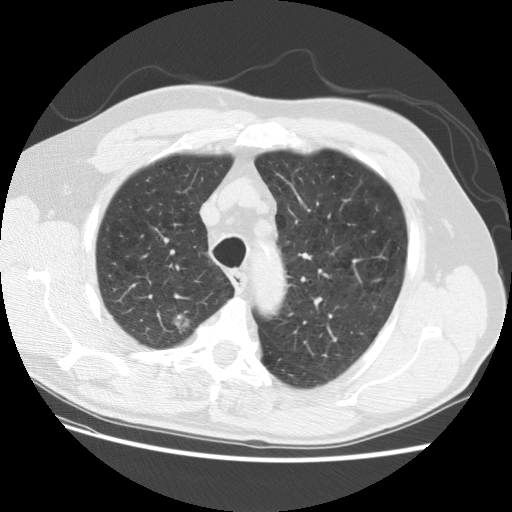
Chest CT (low-dose screening protocol), one axial image; first (baseline) screen; lung window (W 1500 / L -600 HU); 2.5 mm slice thickness; standard (soft-tissue) reconstruction kernel (STANDARD); 140 kVp. Male participant, aged 69 years at enrolment. Former smoker at enrolment.
Lesion marked by an expert reader, box from (x=156, y=305) to (x=203, y=346) px. The exam's reader record, not a measurement of the box and not confirmed to be the same lesion: non-calcified nodule or mass ≥4 mm, right upper lobe, 15 × 15 mm, spiculated (stellate) margins, soft tissue attenuation. Participant outcome: lung cancer diagnosed 22 days after this screen — large cell neuroendocrine carcinoma, right upper lobe, poorly differentiated (G3), stage IA (AJCC 6th edition), 23 mm at pathology.